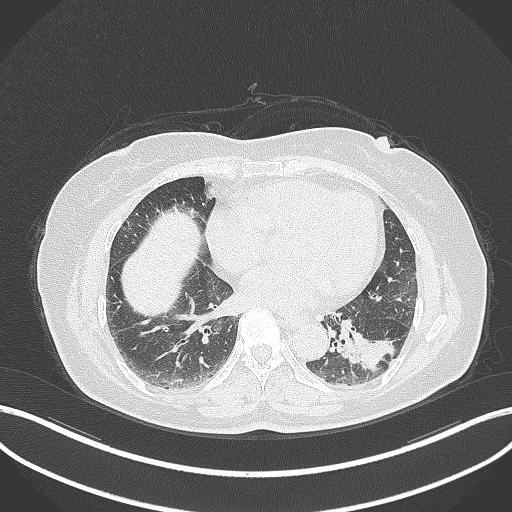
Chest CT, one axial slice; position 150 of 311 along the scan axis; reconstruction kernel B70f; 120 kVp; lung window (W 1500 / L -600 HU); 1 mm slice thickness; 512 × 512 image matrix. Patient: female, 59 years. Case-level facts recorded for this patient, not image findings: clinical TNM (as recorded): T2a N0 M0; histopathological grade: G2-3.
Outlined on this slice (bounding box drawn by a radiologist):
- lung tumour (recorded histology: adenocarcinoma): bounding box (x1, y1, x2, y2) in pixels: (345, 330, 396, 374)